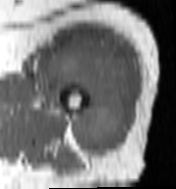
MRI of an extremity soft-tissue mass, one axial slice. Slice 77 of 100 in the series (ordered by position). MR volume resampled by the dataset authors to the PET/CT grid (not the native acquisition matrix). 176 × 189 image matrix. Female patient. From the clinical record (not read from this slice): histological type: undifferentiated – high grade; grade: high; site of the primary tumour: left thigh.
Annotated regions visible in this slice (expert contour drawn on MRI and transferred to this co-registered scan by the dataset authors):
- gross tumour volume including surrounding oedema: bounding box [x1, y1, x2, y2] px = [46, 39, 129, 158]
- gross tumour volume (mass): [48, 45, 129, 158]